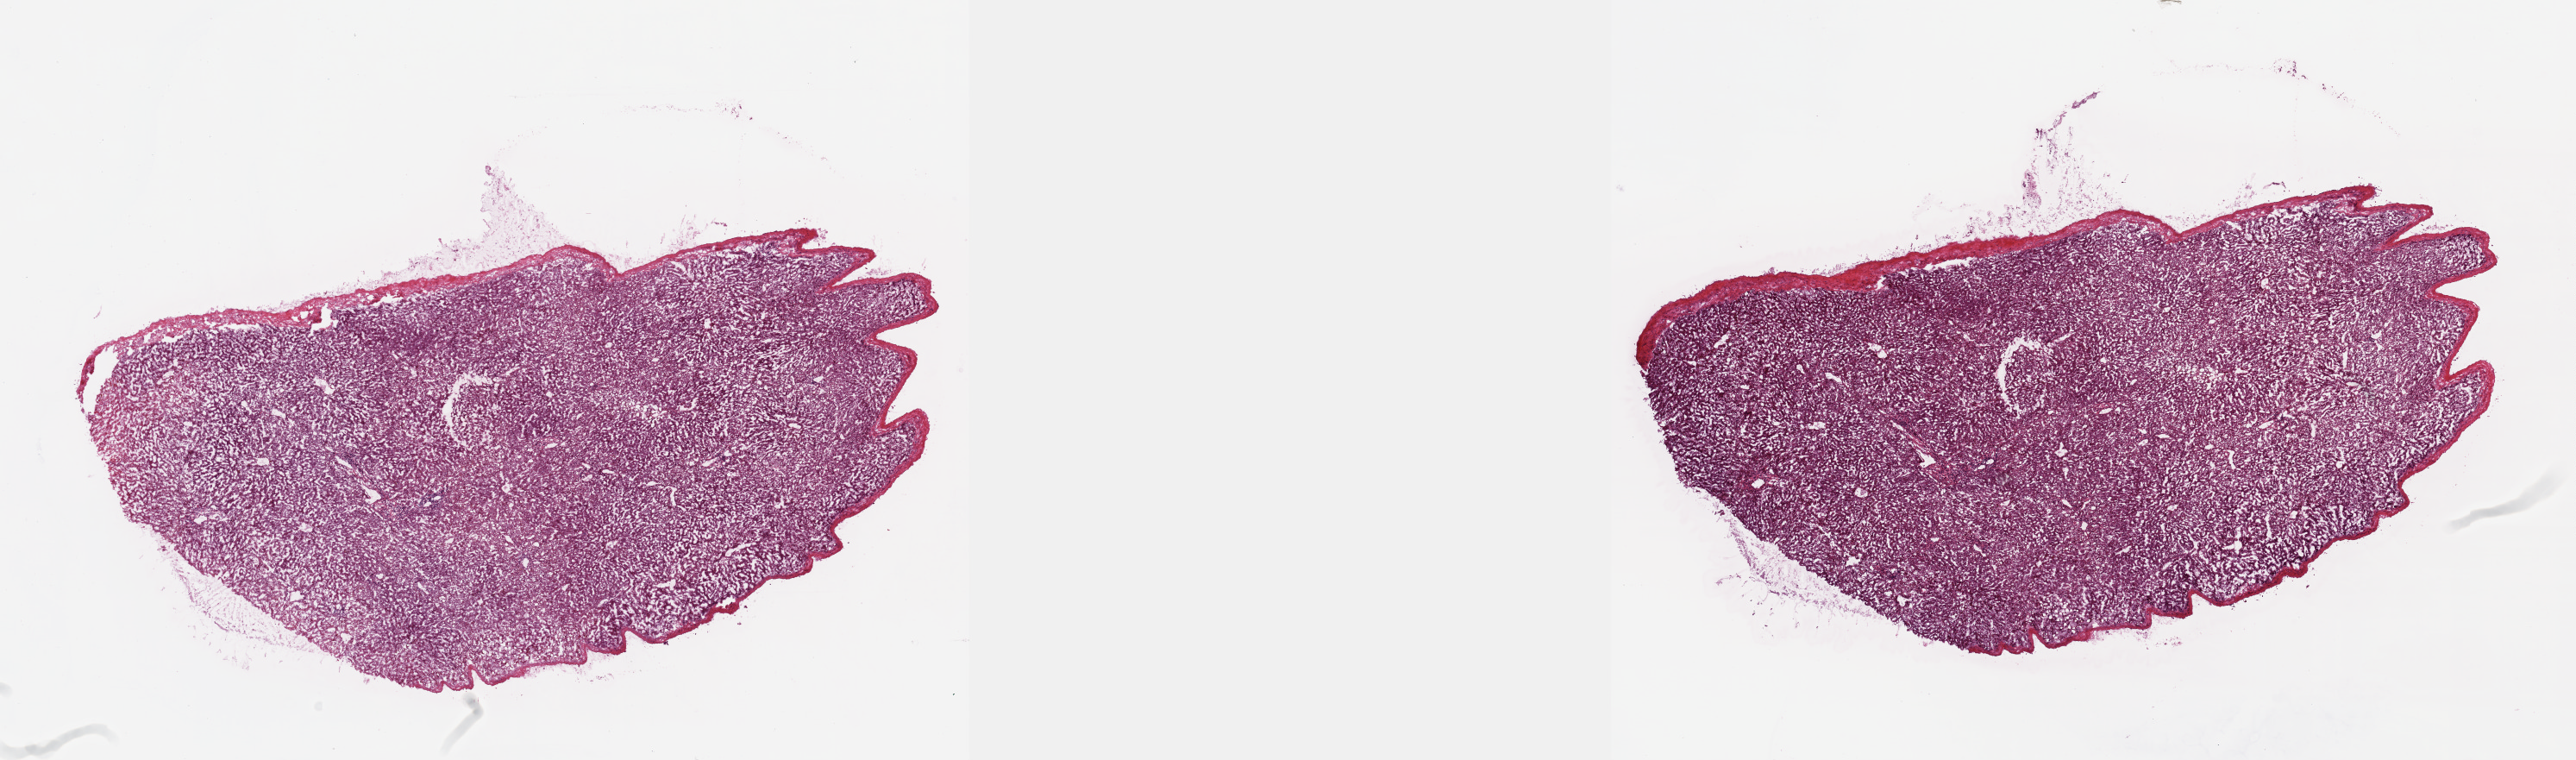
Whole-slide histology image, H&E-stained, a low-resolution overview of the entire scanned area, about 24.1 x 7.1 mm (acquisition: 20x scan), frozen section, sample: solid tissue normal (non-tumour tissue), bile duct. Female, age 74 years at initial diagnosis. Composition of this section per pathologist review: tumour cells 0%, tumour nuclei 0%, normal cells 100%, stromal cells 0%, necrosis 0%. Infiltration values recorded for this section: lymphocyte infiltration 0%, monocyte infiltration 0%, neutrophil infiltration 0%.
This section: solid tissue normal sample (biorepository sample class). Patient diagnosis: Cholangiocarcinoma (intrahepatic bile duct).